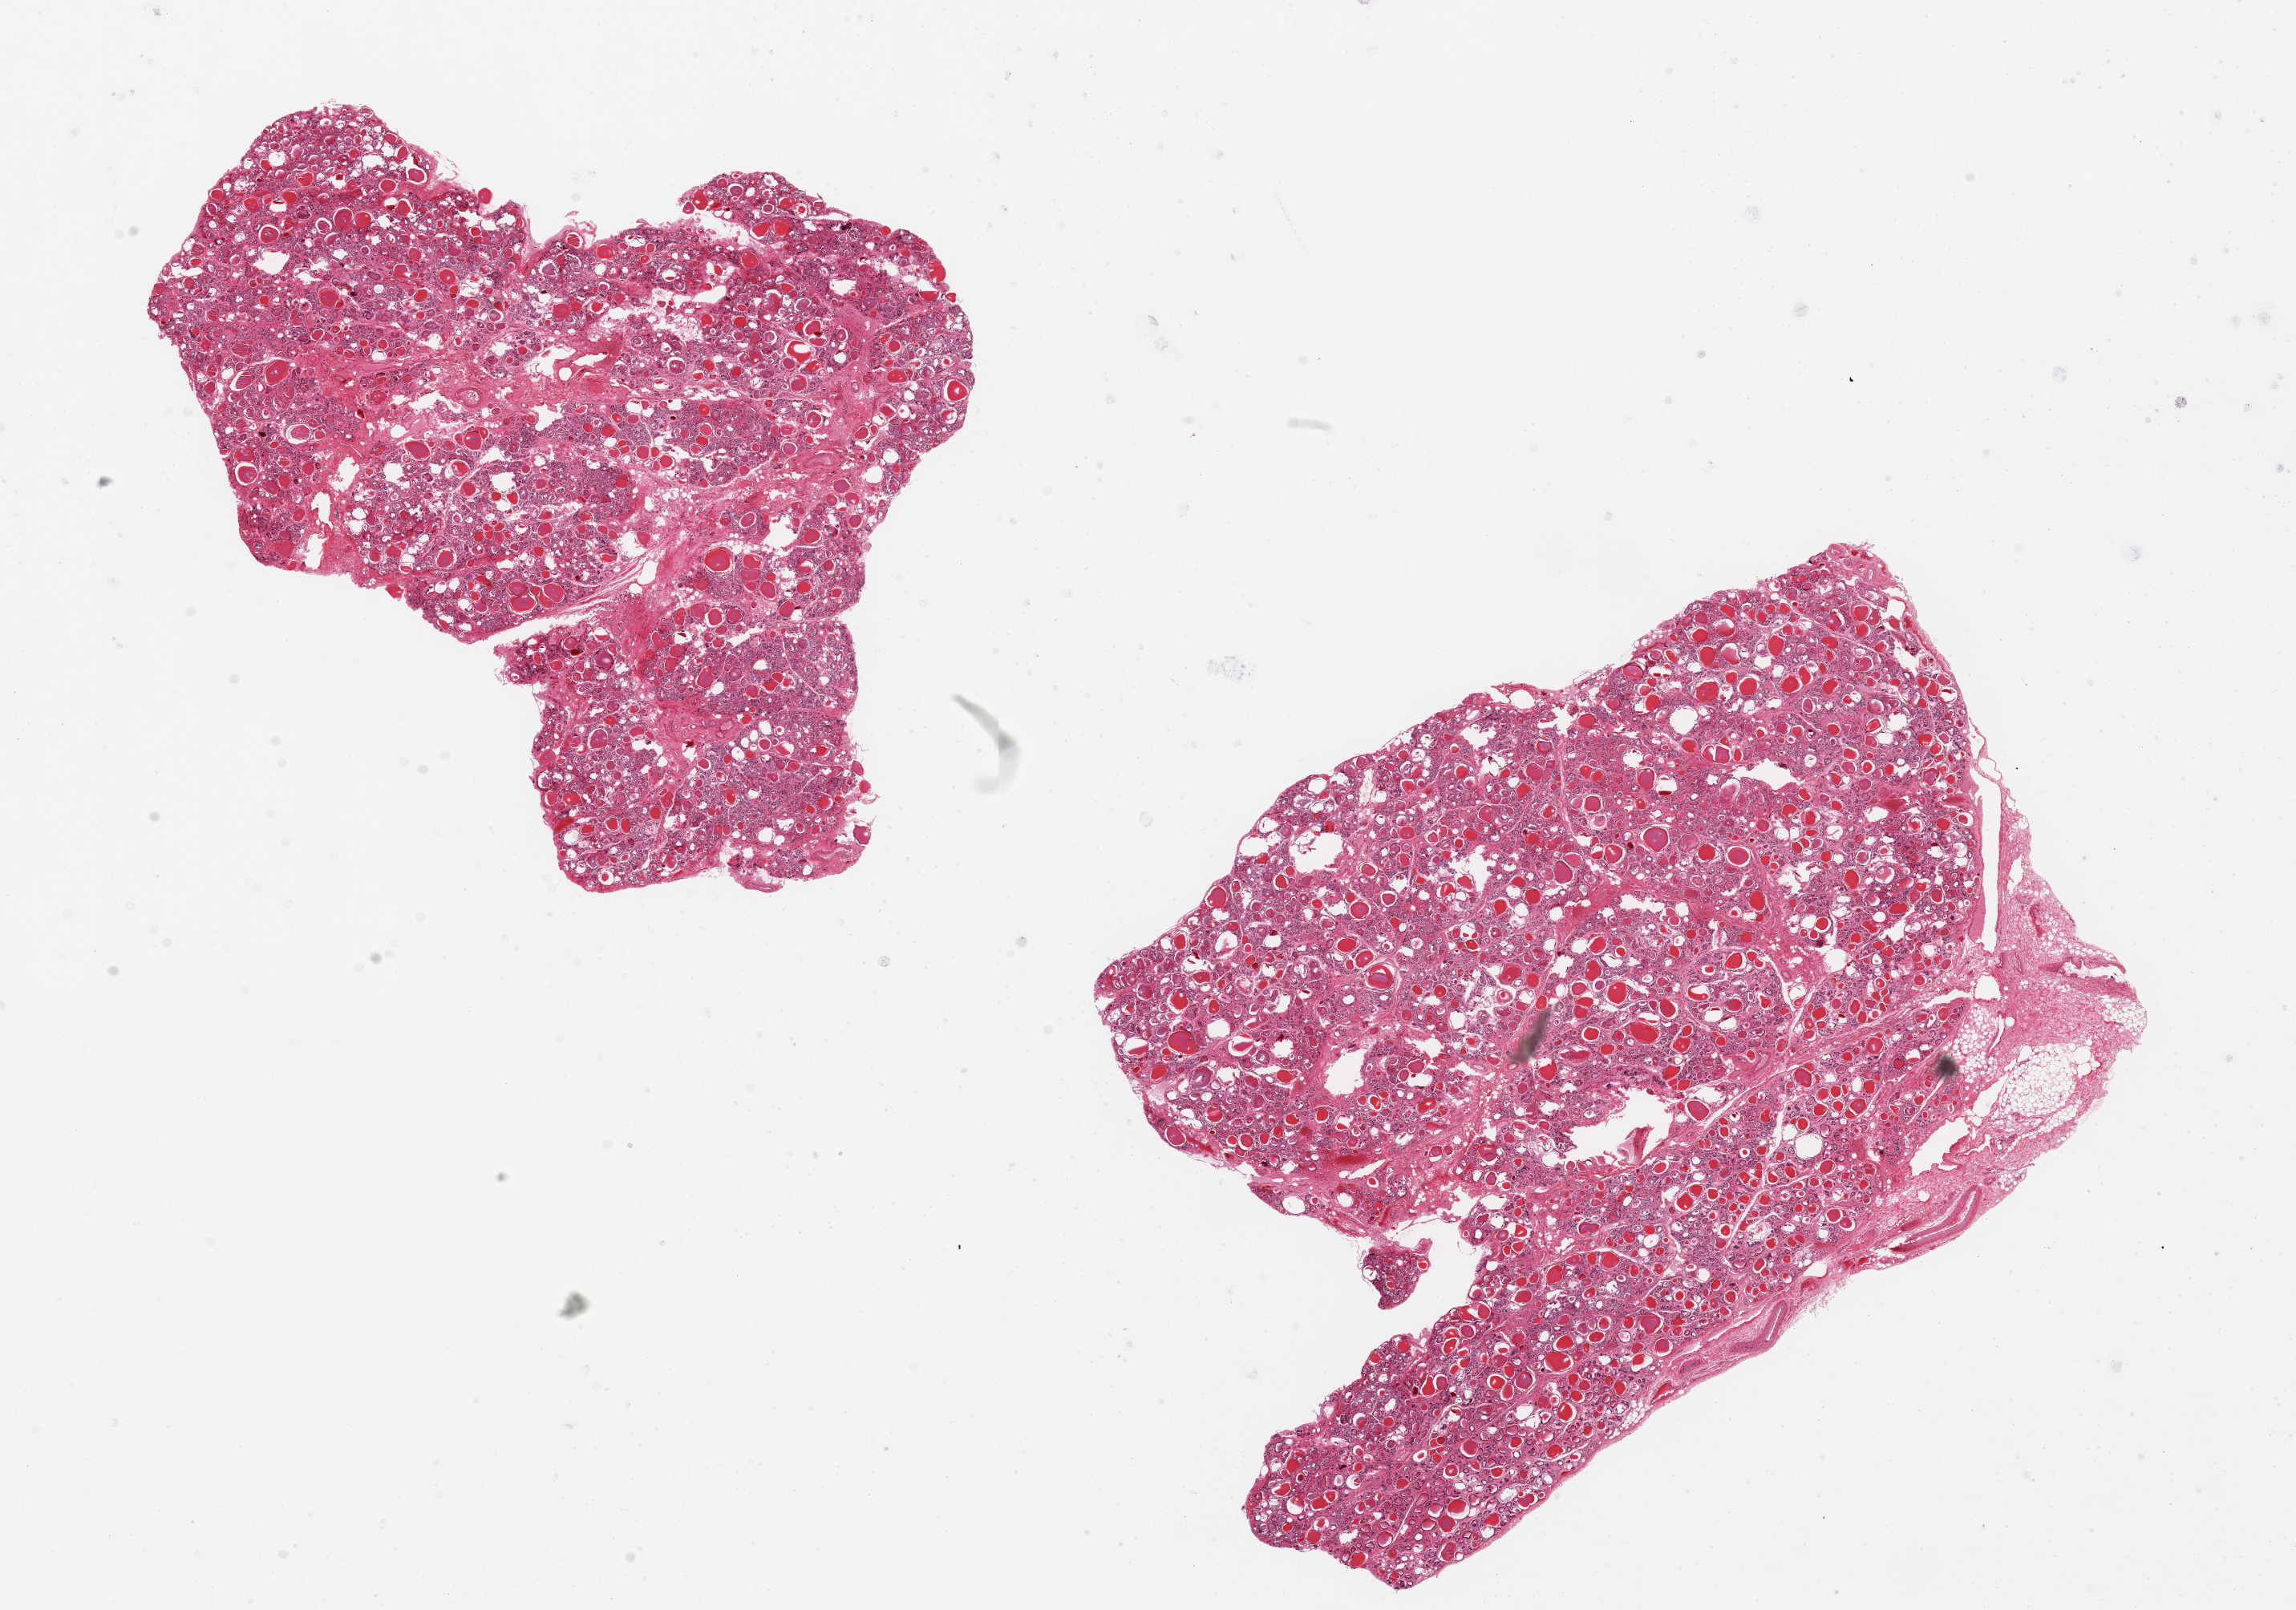
Digitized haematoxylin and eosin-stained section, low-resolution overview of the scanned area, about 22.6 x 15.9 mm. PAXgene-fixed, paraffin-embedded tissue. Section of thyroid (target tissue). Tissue donor sample. Donor sex: female.
- pathologist's review note for this sample: 2 ~8.5x6mm aliquots, regressive changes noted